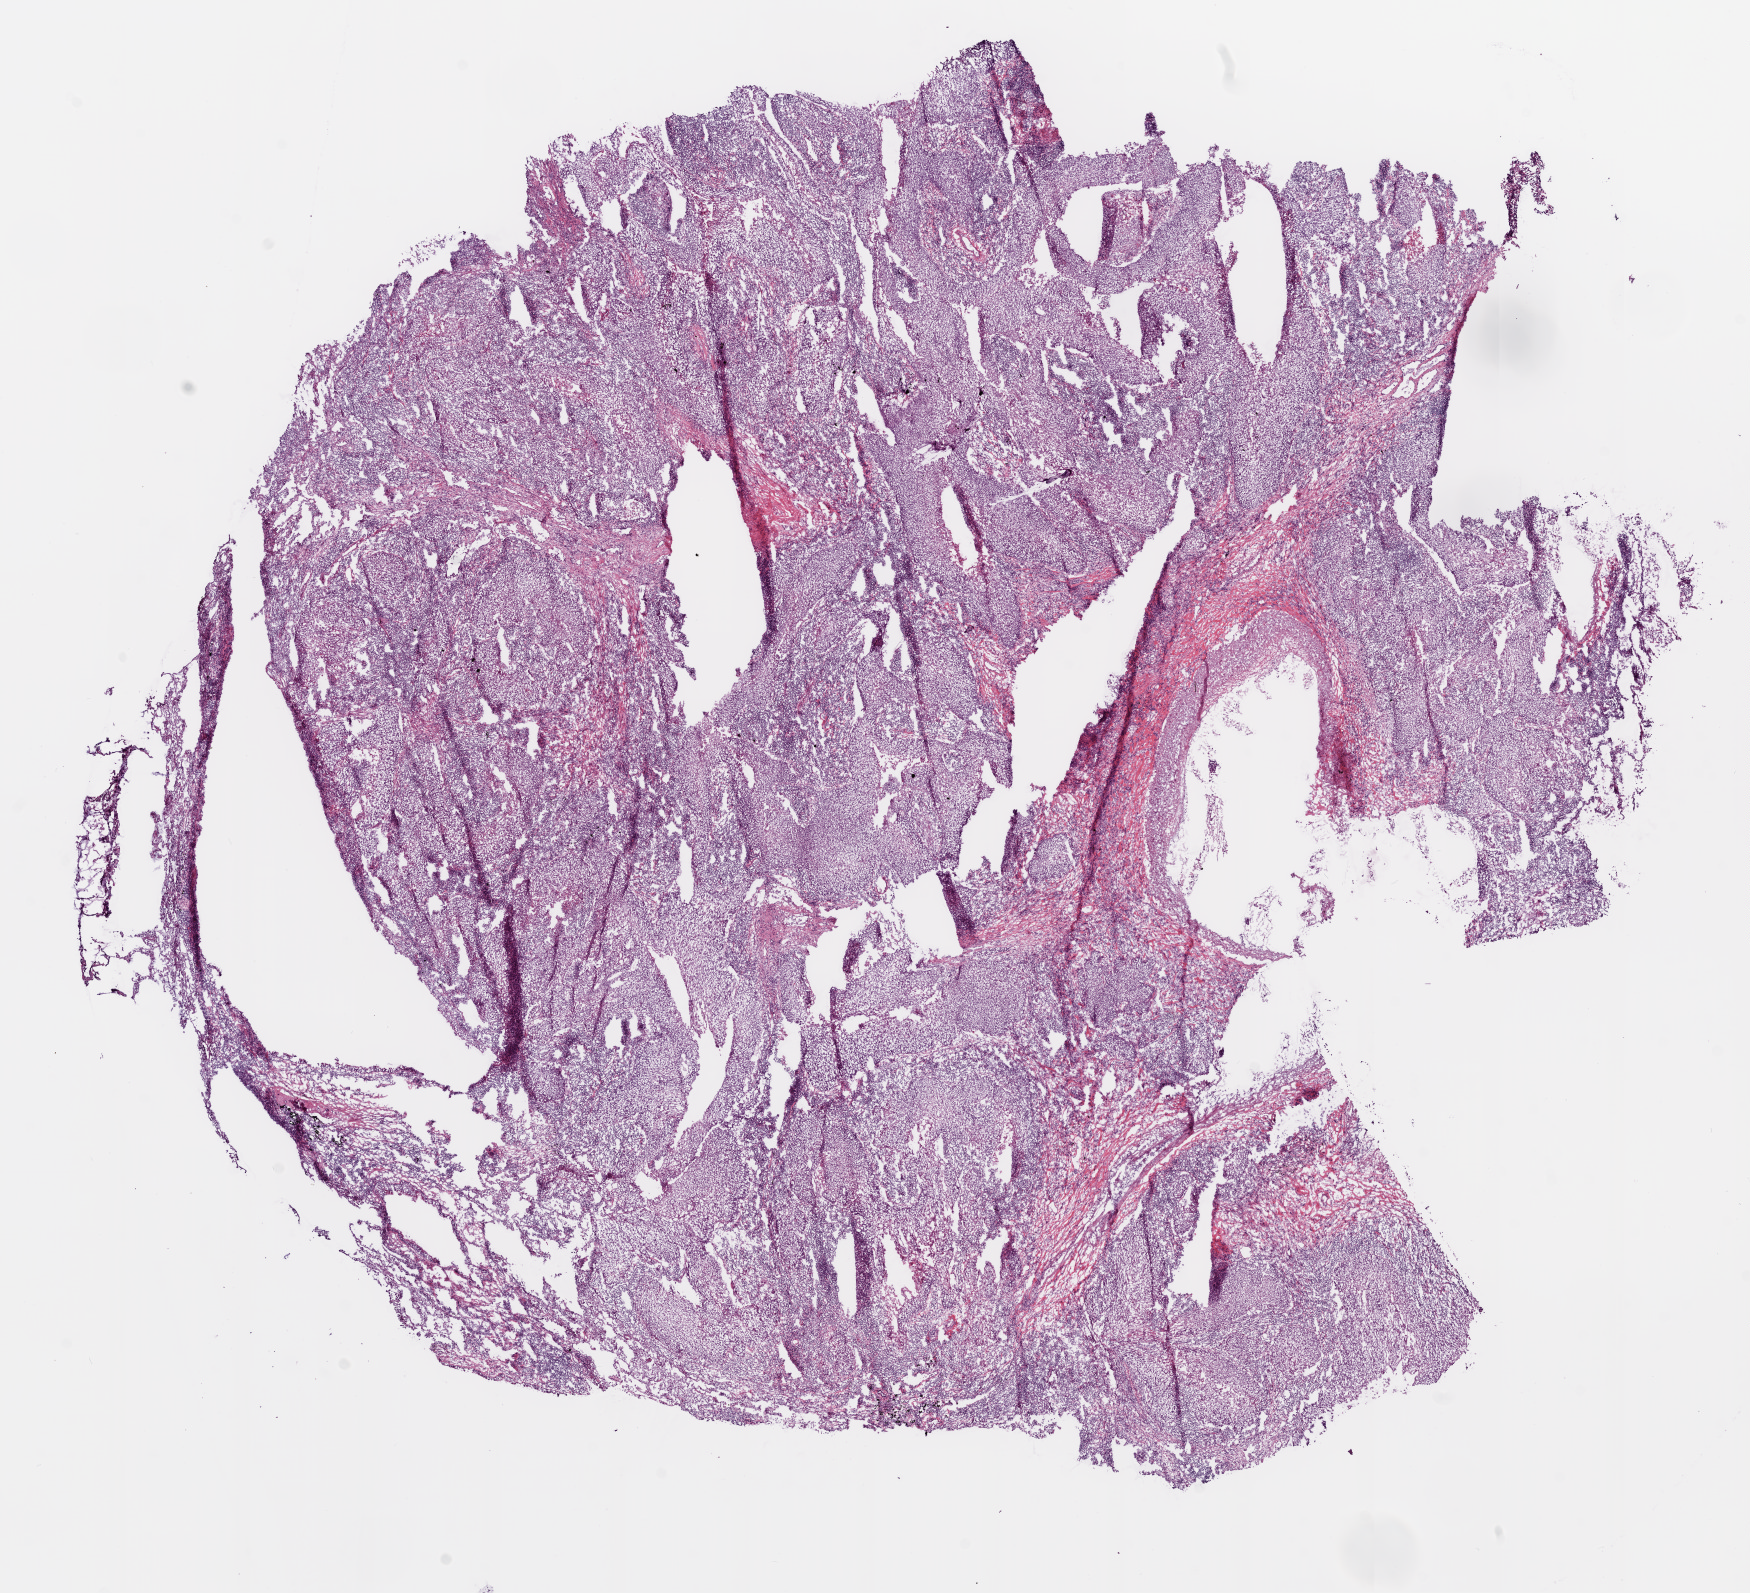
Whole-slide histology image, H&E — low-resolution overview of the scanned area, about 14.0 x 12.8 mm, frozen section from the bottom of the tissue portion, sample: primary tumour, lung. Female, age 75 years at initial diagnosis. Pathologist review of this section (percent, as recorded): tumour cells 89%, tumour nuclei 80%, normal cells 3%, stromal cells 5%, necrosis 3%.
• AJCC pathologic stage: IIA (6th edition)
• laterality: left
• diagnosis: Squamous cell carcinoma, NOS (upper lobe, lung)